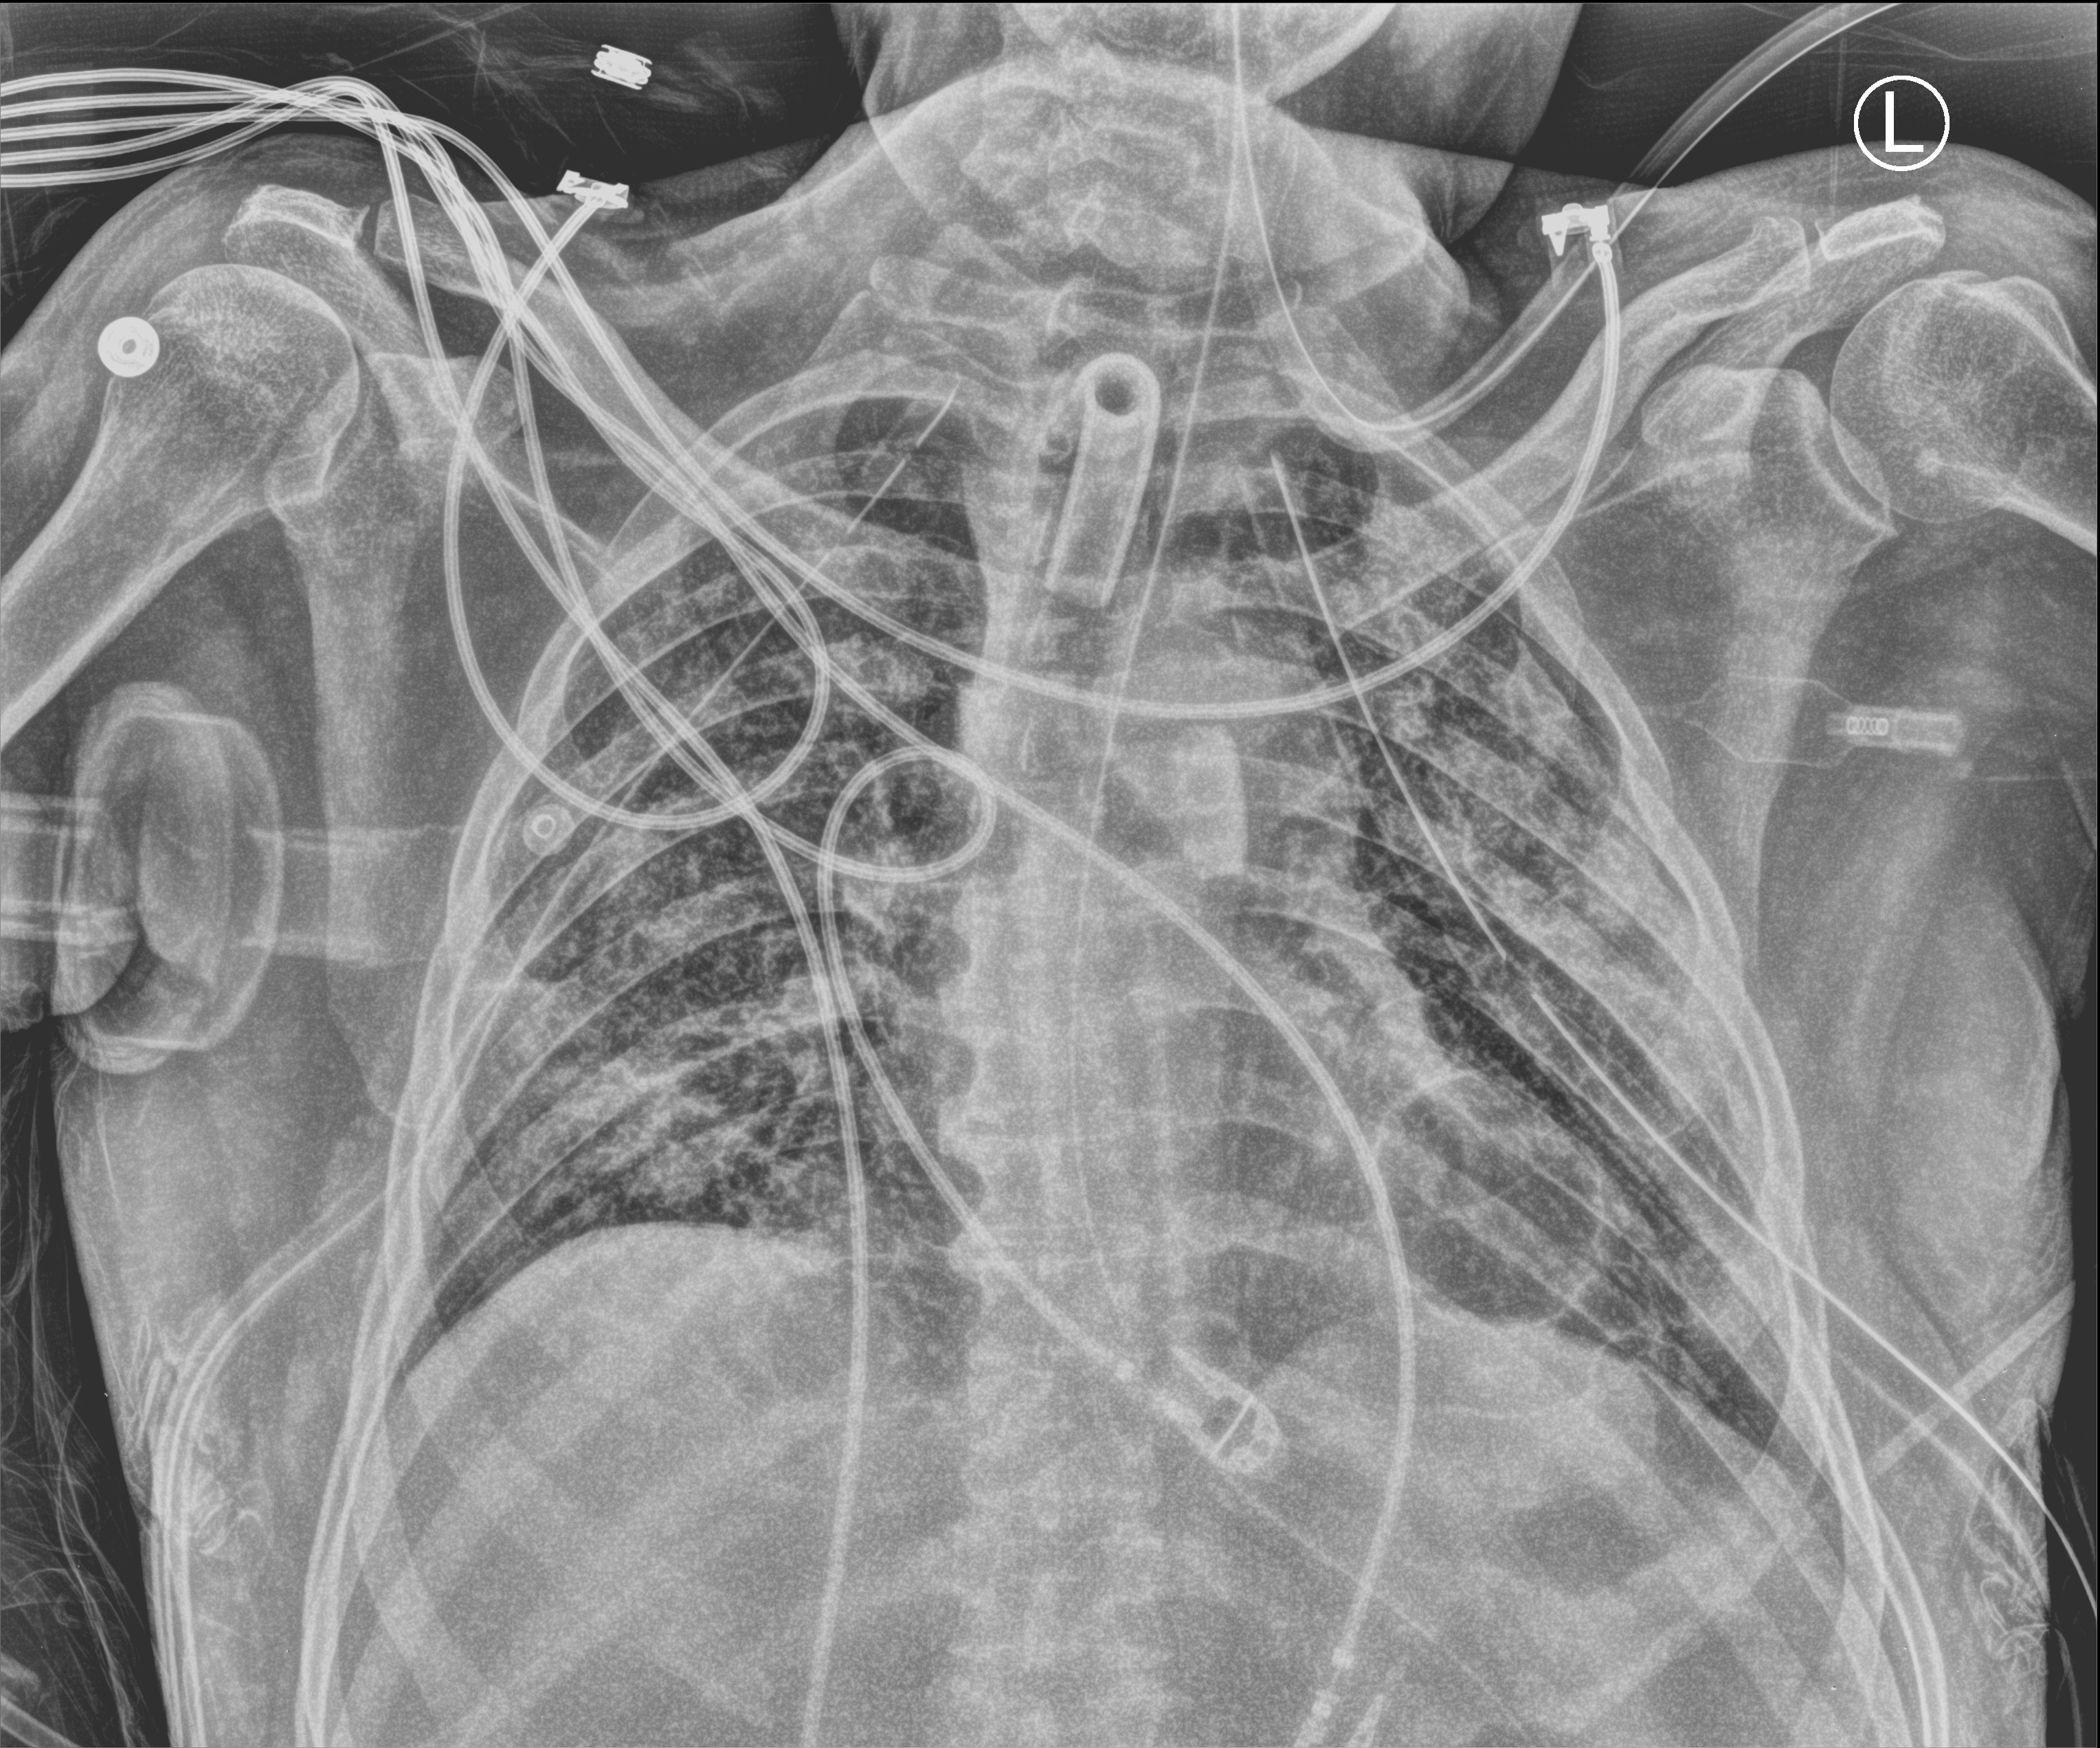
Bedside chest radiograph (computed radiography); anteroposterior (AP) projection. Patient hospitalised with COVID-19; male, aged 18–59 years.
Hospital-stay facts (about this admission, not read from this image; timing relative to this image not recorded): mechanically ventilated during this hospital stay: yes; admitted to intensive care during this hospital stay: yes; length of hospital stay: 83 days.